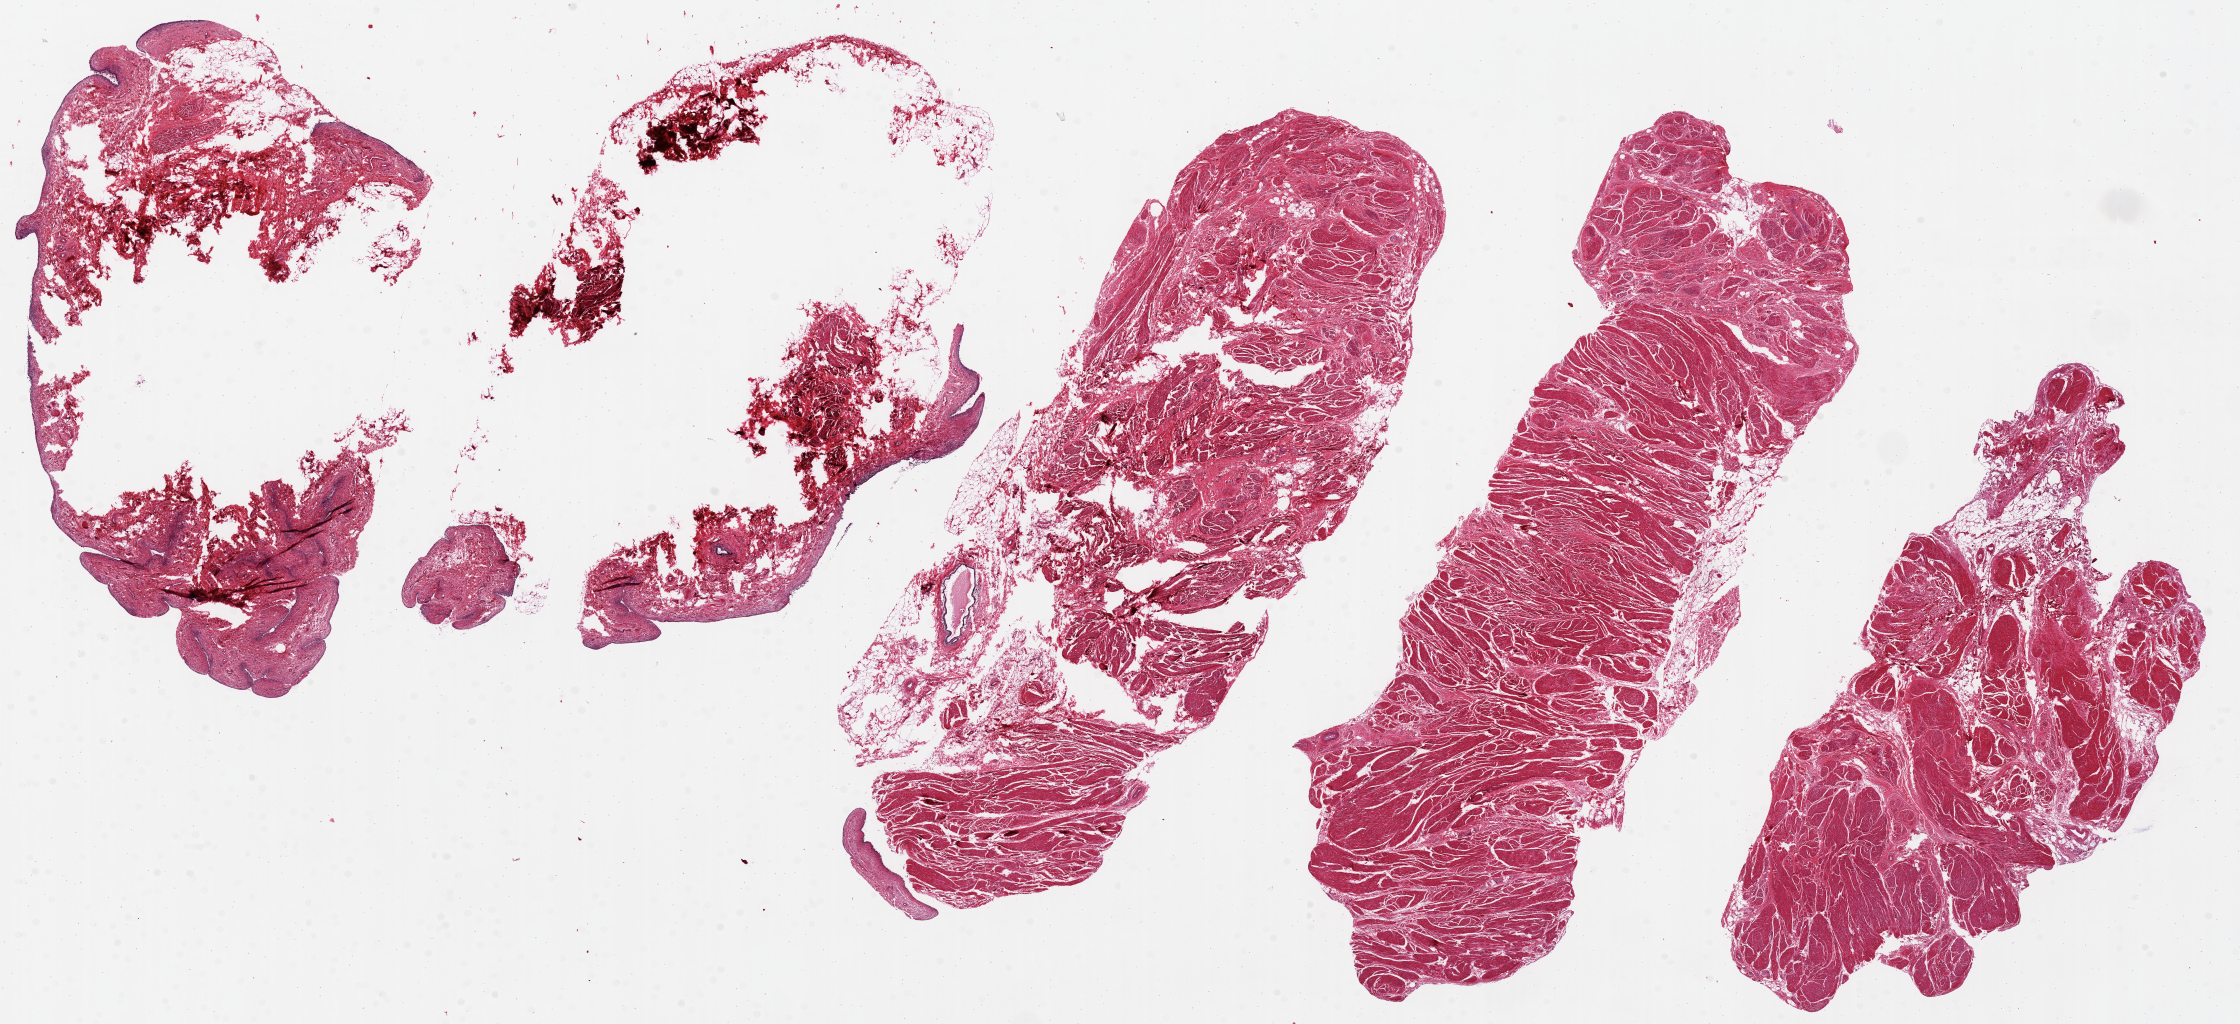
Digitized haematoxylin and eosin-stained section — low-resolution overview of the scanned area, about 35.4 x 16.2 mm, PAXgene-fixed, paraffin-embedded tissue, sampled site (target tissue): urinary bladder, donor tissue sample.
- pathologist's review note for this sample: Two of five sections poorly fixed/extreme separation. Mucosa sub-totally sloughed/degraded, about 31 microns thick where present